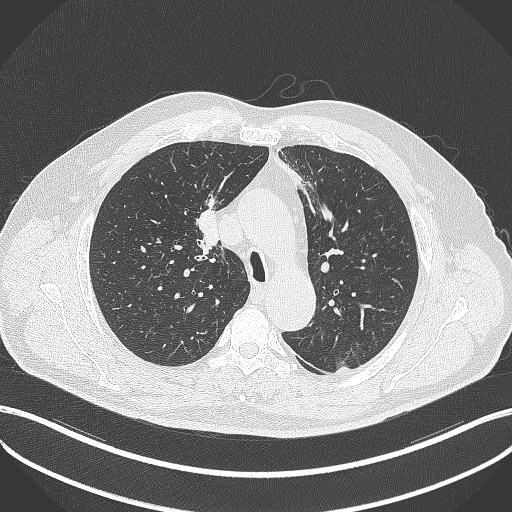
Chest CT, one axial slice; reconstruction kernel B70f; lung window (W 1500 / L -600 HU); 1 mm slice thickness; 512 × 512 image matrix. Male patient, age 60 years. From the clinical record (not read from this slice): clinical TNM (as recorded): T1b N1 M0.
Annotated regions visible in this slice (bounding box drawn by a radiologist):
- lung tumour (recorded histology: squamous cell carcinoma): bounding box [x1, y1, x2, y2] px = [194, 204, 223, 251]